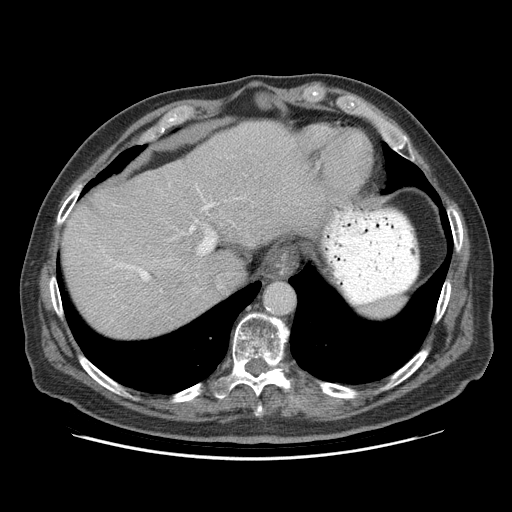
Contrast-enhanced abdominal CT (liver protocol), one axial slice; position 73 of 95 along the scan axis; reconstruction kernel STANDARD; 140 kVp; soft-tissue window (W 400 / L 40 HU); 2.5 mm slice thickness; 512 × 512 image matrix, field of view 400 × 400 mm. From the clinical record (not read from this slice): diagnosis: hepatocellular carcinoma (patient treated with transarterial chemoembolisation; whether this scan precedes or follows treatment is not stated here); TNM stage (as recorded): Stage-IVB; Child-Pugh class: A; tumour nodularity: uninodular.
Annotated regions visible in this slice (semi-automatic segmentation, software-assisted and operator-edited):
- abdominal aorta: bounding box (x1, y1, x2, y2) in pixels: (265, 283, 293, 313)
- liver parenchyma outside the tumour (the mass and vessels are separate outlines, so this box may not span the whole liver): (64, 120, 320, 338)
- liver vessels: (127, 204, 212, 280)